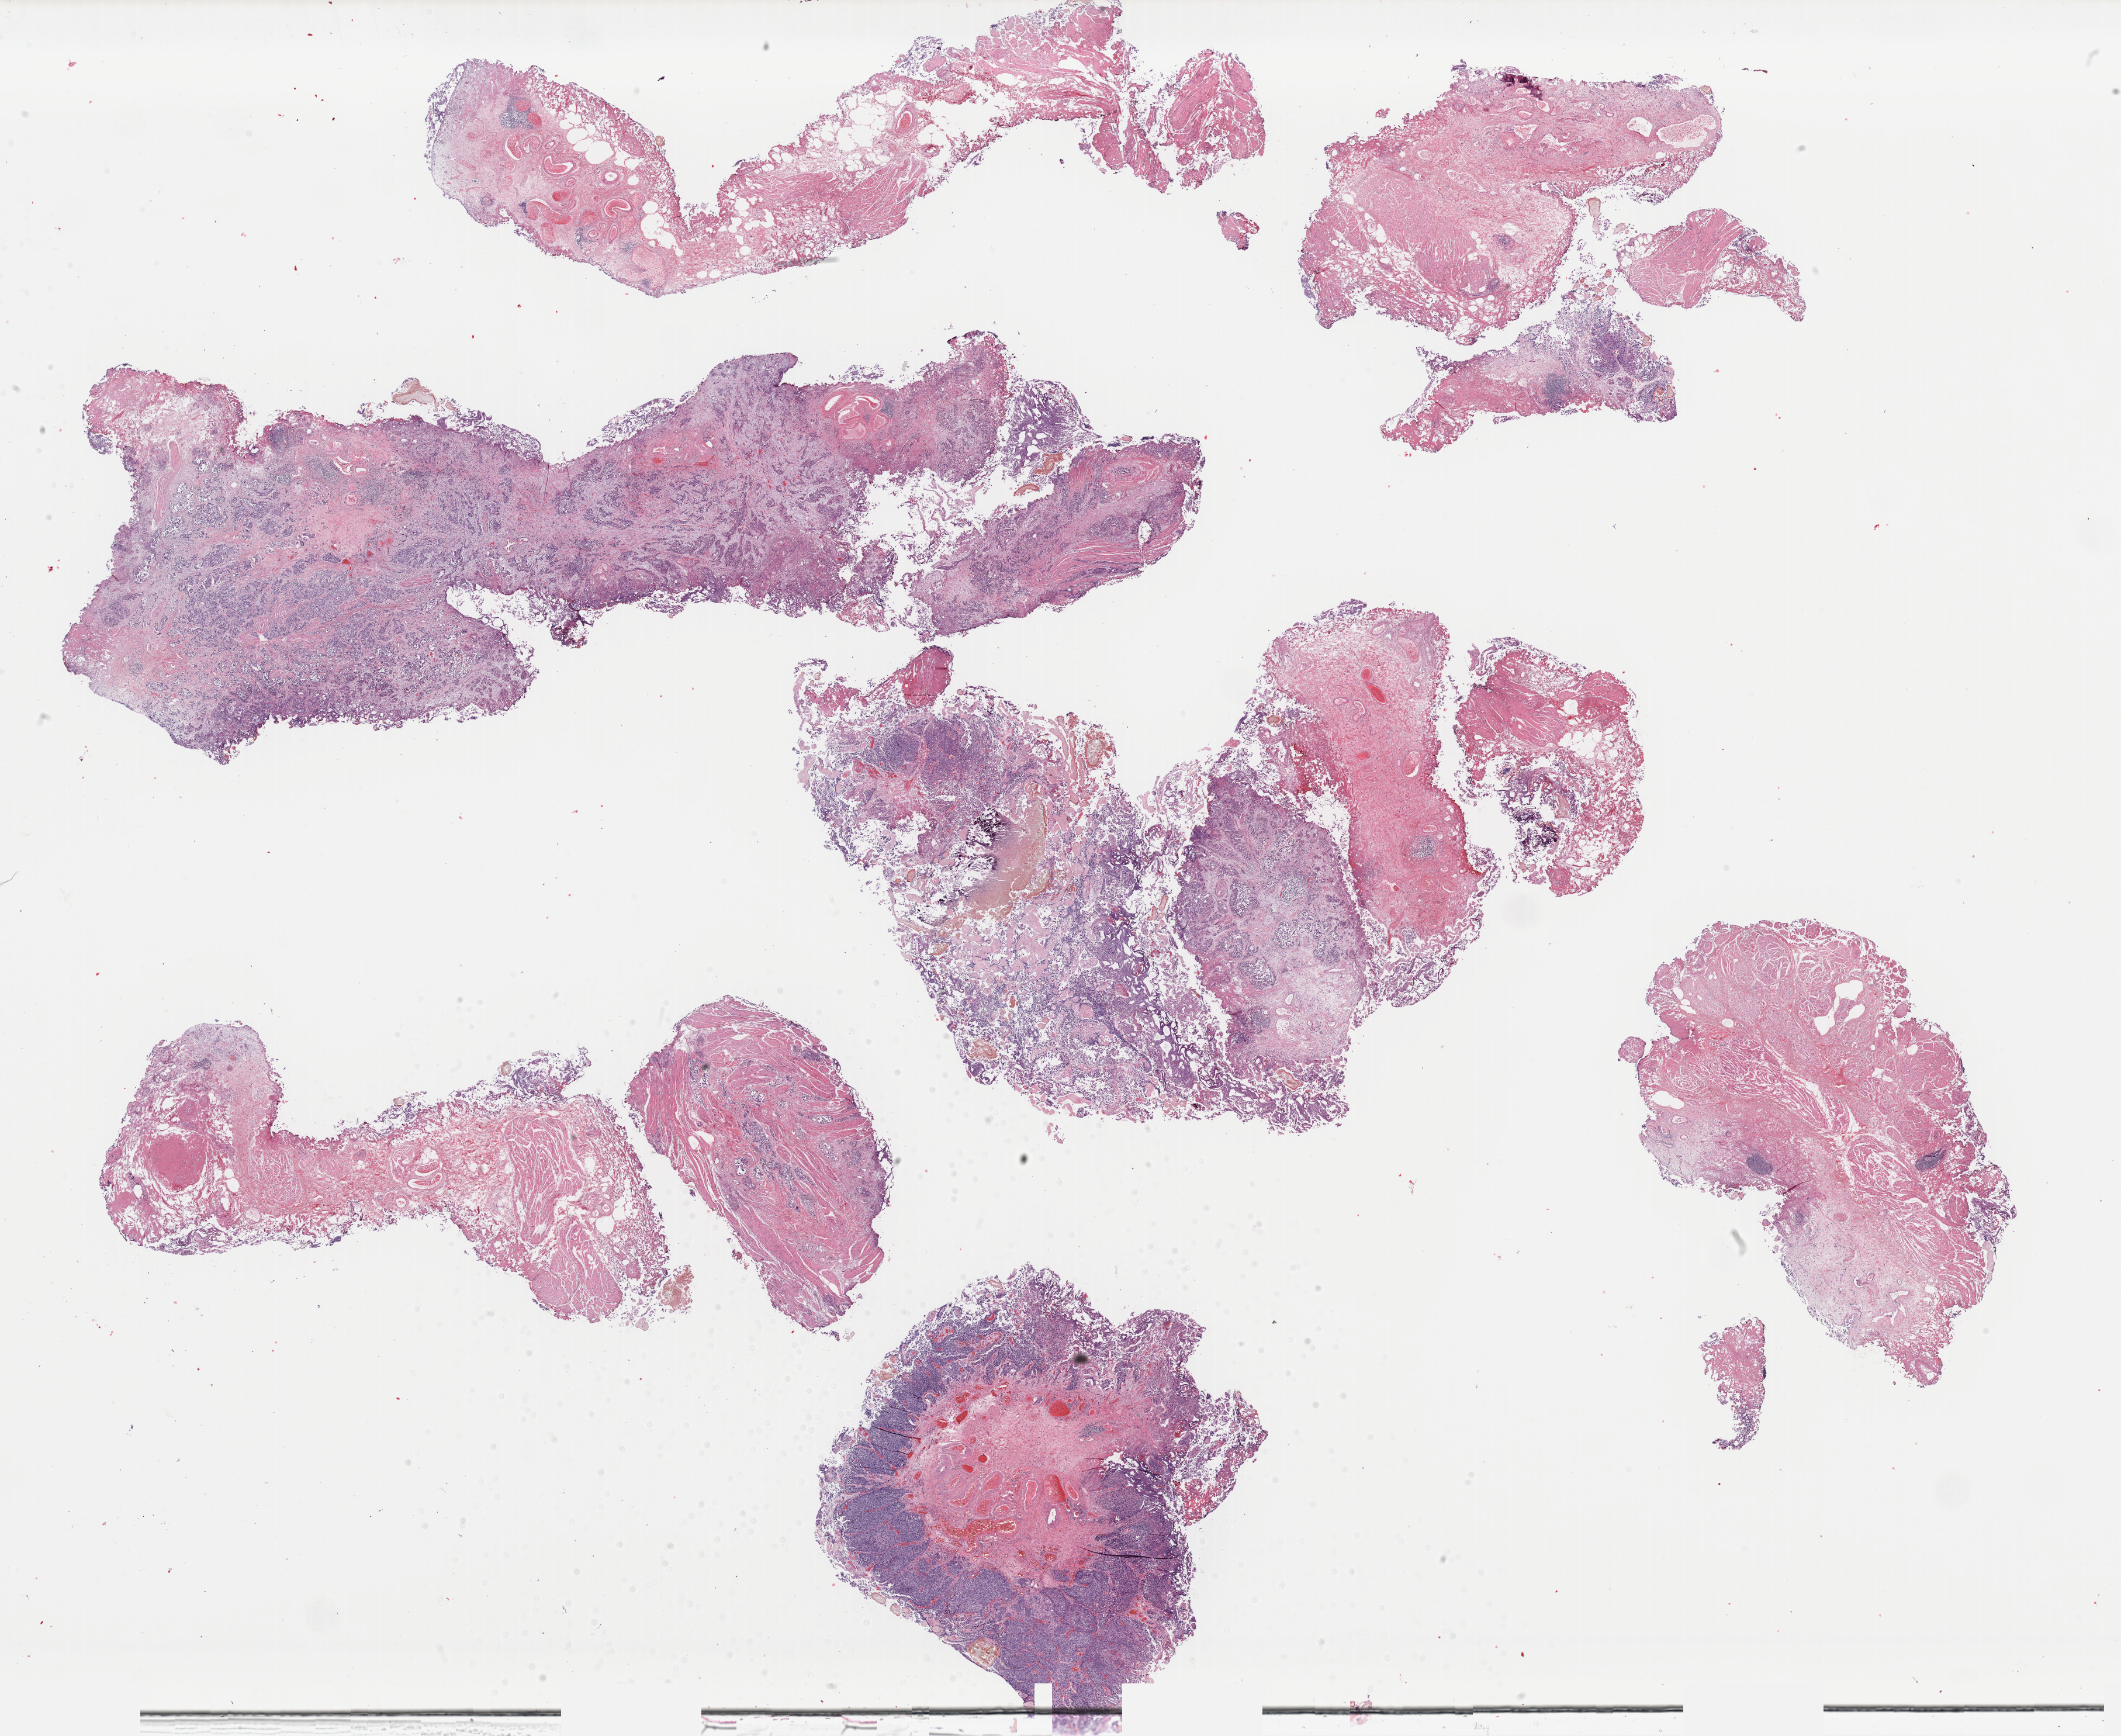
Hematoxylin and eosin (H&E) stained whole-slide image — whole scanned area (about 28.7 x 23.5 mm, slide scanned at 40x) shown as a low-resolution overview, formalin-fixed paraffin-embedded (FFPE) diagnostic section, primary tumour sample from the bladder. Male, age 72 years at initial diagnosis. Histologic grade: high grade.
• lymph nodes positive (case pathology): 0 of 27 examined
• AJCC pathologic stage: II
• pathologic diagnosis: Transitional cell carcinoma